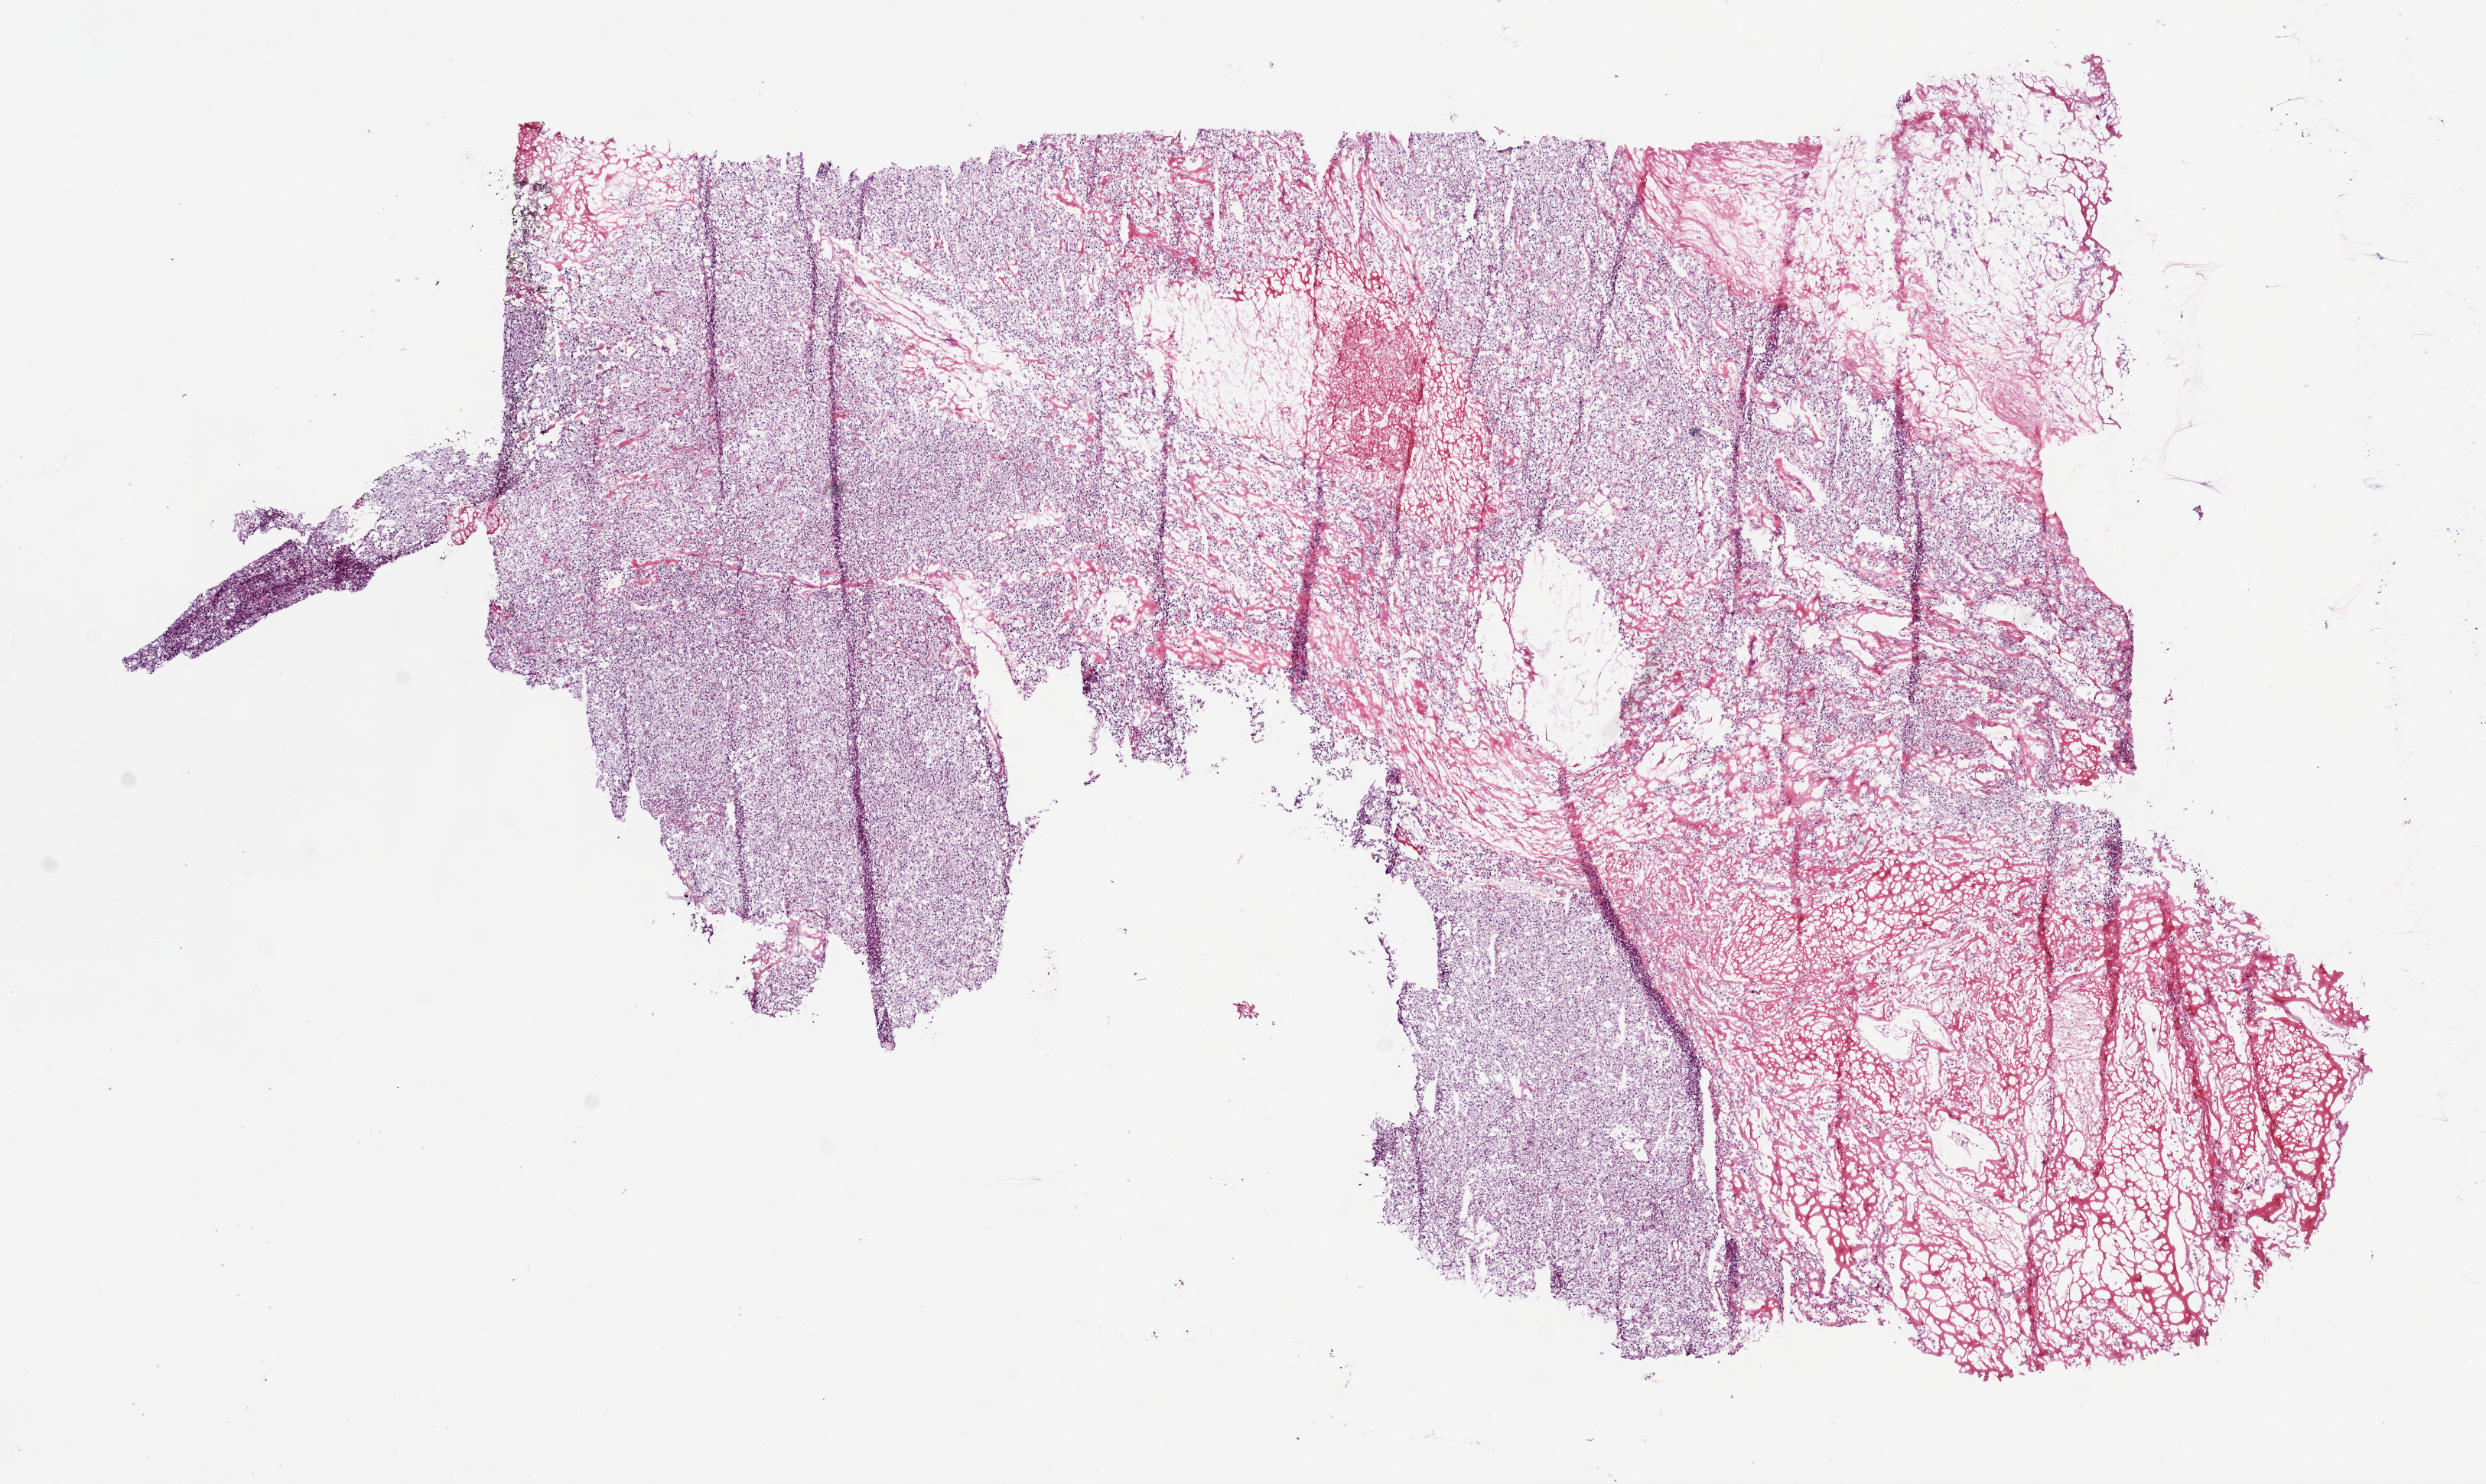
Digitized H&E-stained tissue section (whole slide), shown as a low-resolution overview of the whole scanned area (about 13.0 x 7.8 mm, from a 20x scan); frozen section from the bottom of the tissue portion; kidney, primary tumour sample. Patient: male, age at initial diagnosis 69 years. Histologic grade: G3 (poorly differentiated). Slide review estimates, as recorded: tumour cells 75%, tumour nuclei 80%, normal cells 0%, stromal cells 25%, necrosis 0%.
- AJCC pathologic stage: I
- histologic diagnosis: Clear cell adenocarcinoma, NOS